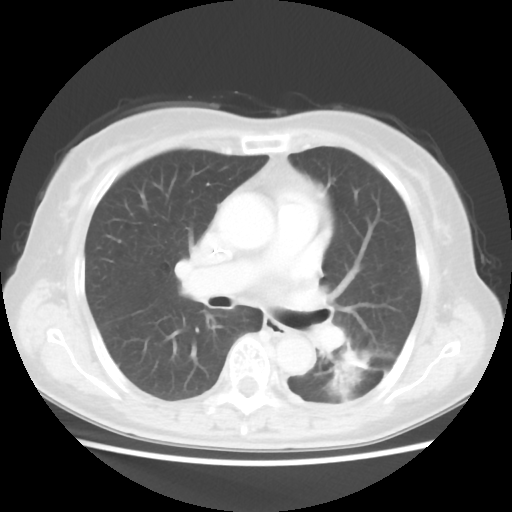
Chest CT, one axial slice. Slice 21 of 40 in the series (ordered by position). 100 kVp. Lung window (W 1500 / L -600 HU). 5 mm slice thickness. 512 × 512 image matrix, field of view 341 × 341 mm. Female patient, age 69 years. From the clinical record (not read from this slice): clinical TNM (as recorded): T1c N0 M0.
Structures marked on this image (bounding box drawn by a radiologist):
- lung tumour (recorded histology: adenocarcinoma): bounding box (x1, y1, x2, y2) in pixels: (331, 342, 366, 398)